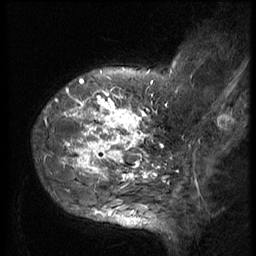
Breast MRI (dynamic contrast-enhanced), one sagittal slice. Slice 13 of 56 in the series (ordered by position). 3 images stored at this slice position (order not interpretable as contrast timing). 1.5 T. TE 4.2 ms, TR 9 ms. 256 × 256 image matrix, field of view 180 × 180 mm. Female patient, age 49 years. Case-level facts recorded for this patient, not image findings: setting: breast cancer imaged before/during neoadjuvant chemotherapy; receptor status: HER2-positive.
Outlined on this slice (semi-automatic segmentation, software-assisted and operator-edited):
- analysis volume of interest (the breast-tissue region the enhancement analysis was run in; not a lesion): bounding box <37,85,160,207> (left, top, right, bottom; pixels)
- tumour enhancement mask (voxels above the 140 % enhancement threshold inside the analysis volume of interest): <45,91,154,182>